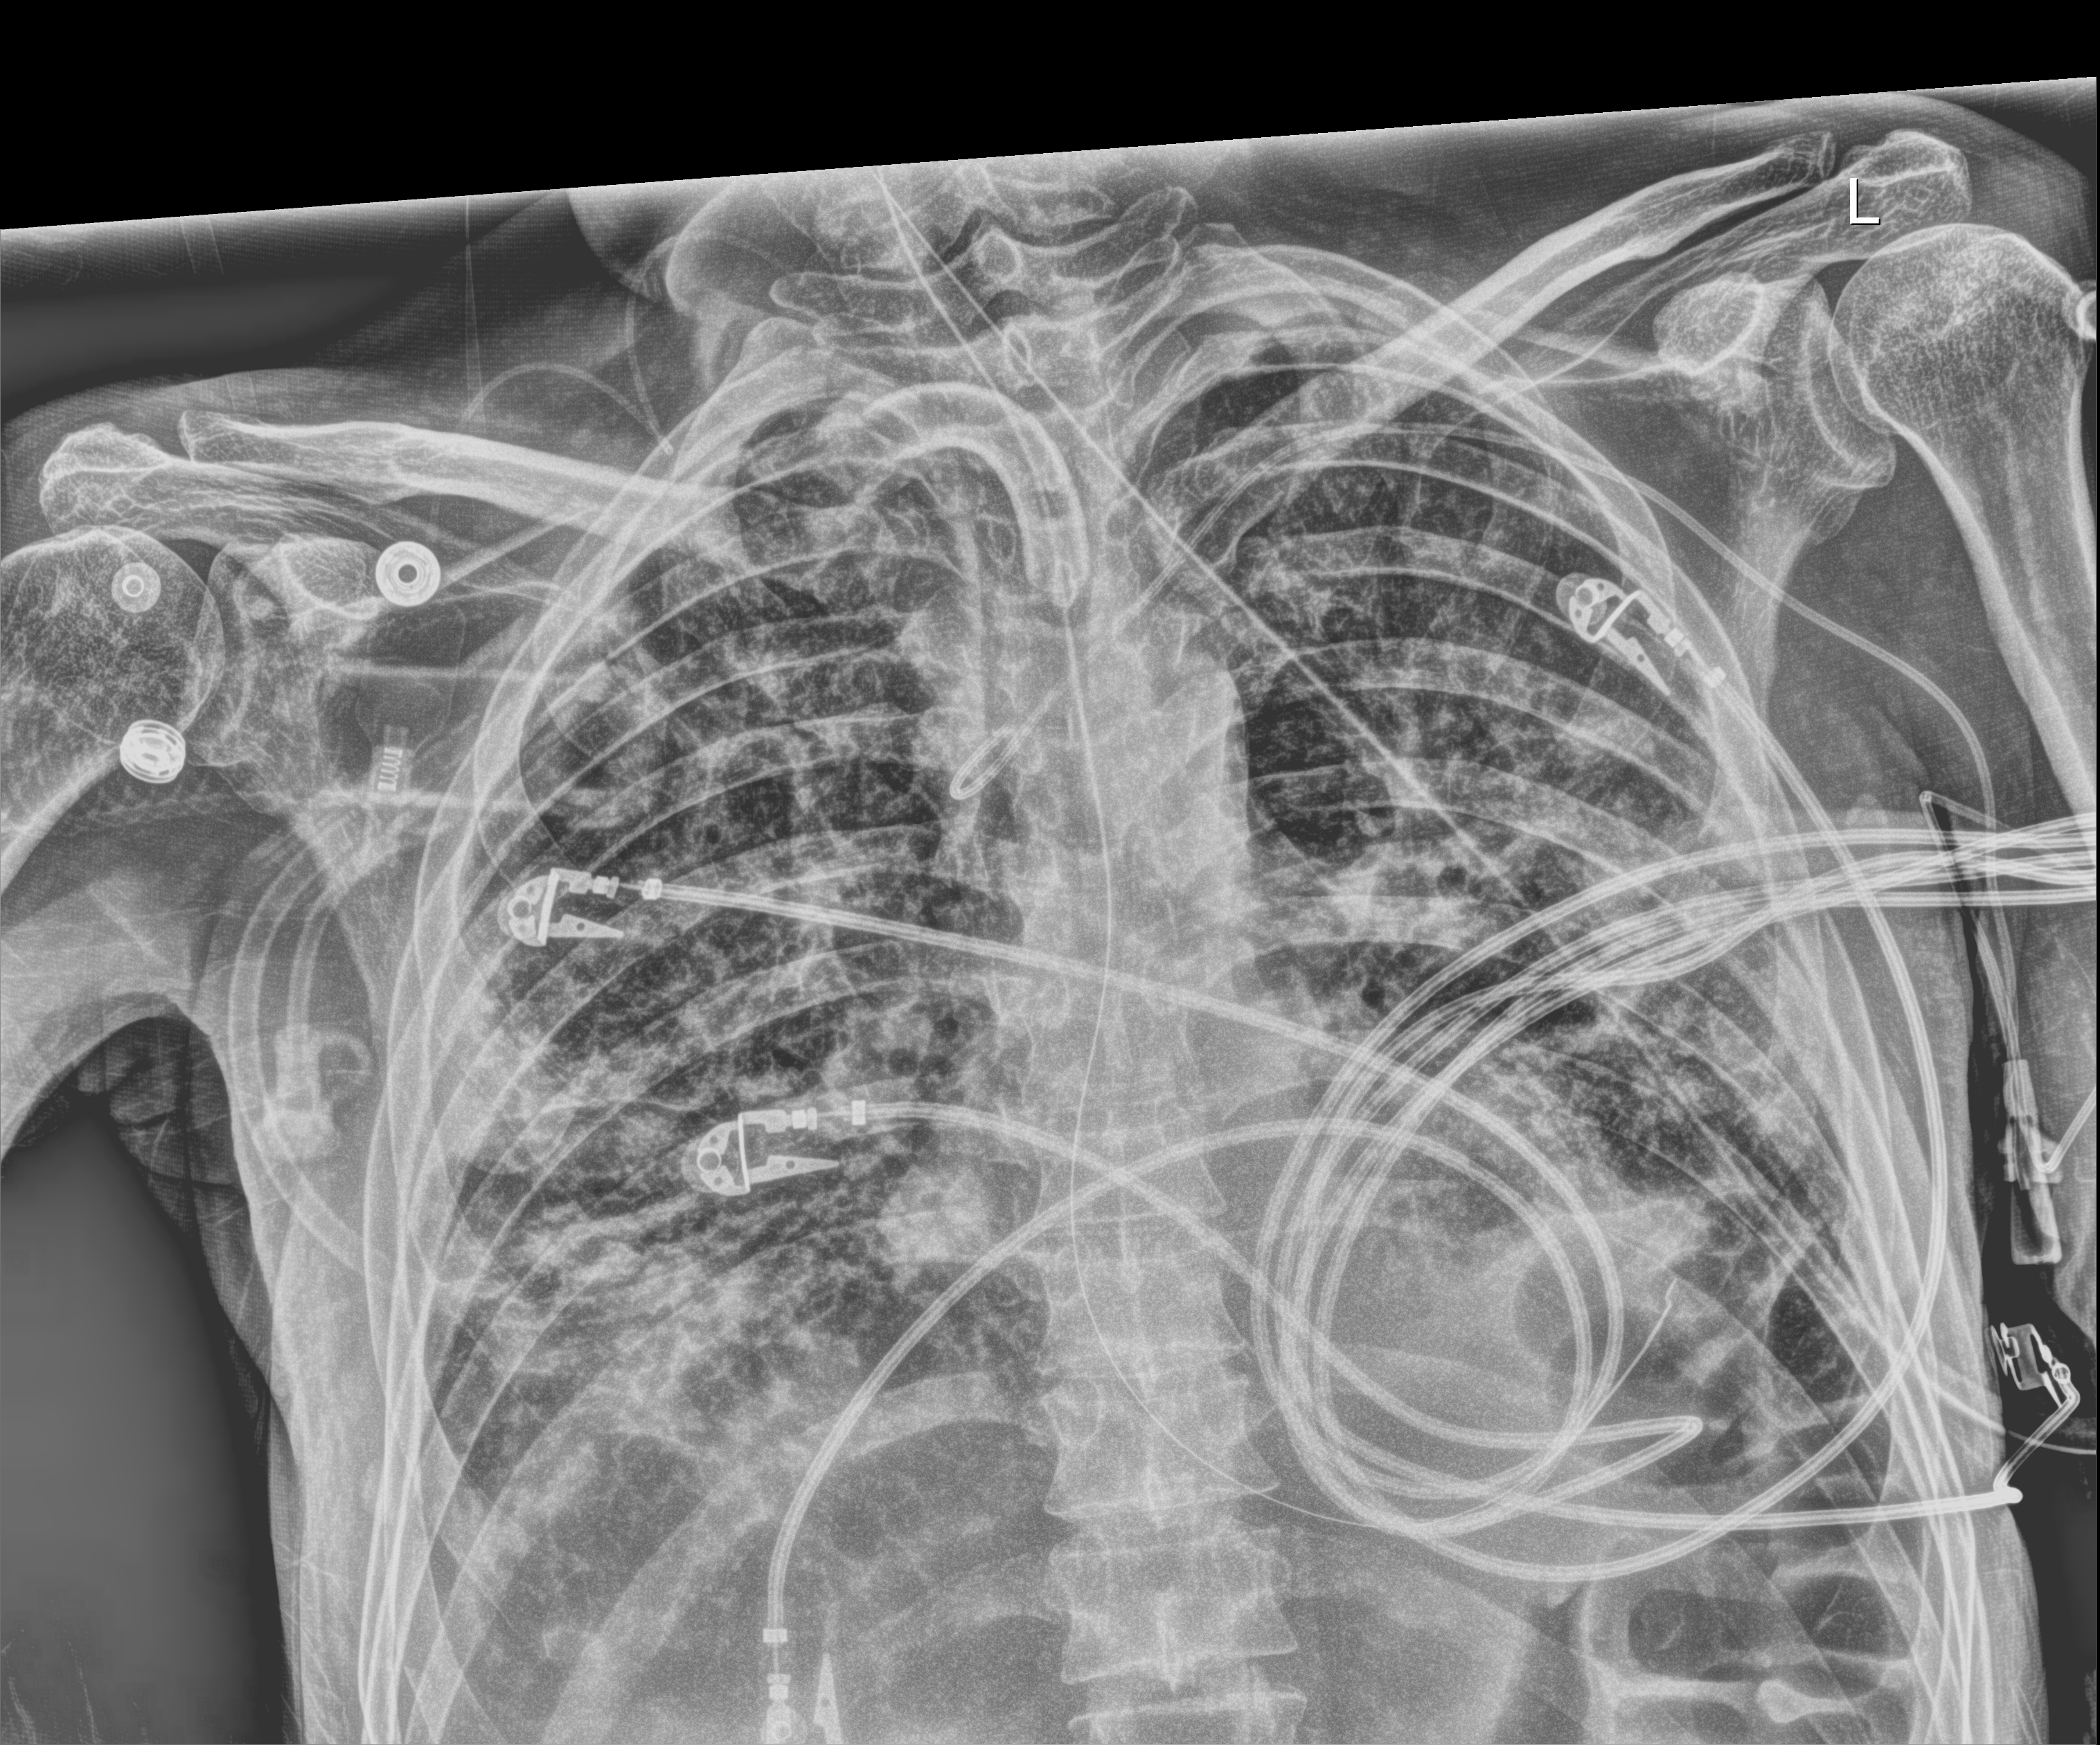
Chest radiograph (digital radiography), anteroposterior (AP) projection. Patient hospitalised with COVID-19; male, aged 18–59 years.
Hospital-stay facts (about this admission, not read from this image; timing relative to this image not recorded): chronic kidney disease (admission record): no.